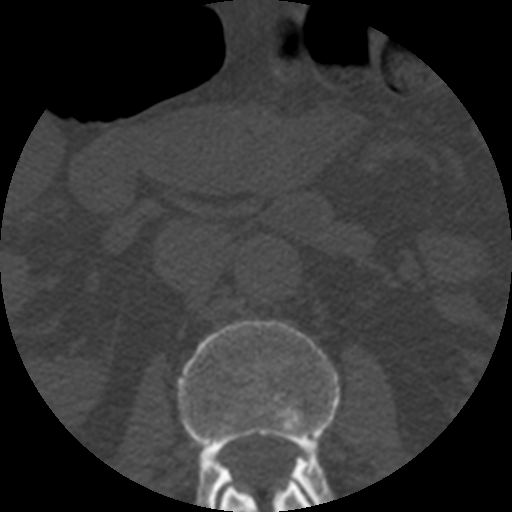
CT including the spine, one axial slice; position 163 of 508 along the scan axis; 120 kVp; bone window (W 1800 / L 400 HU); 1.25 mm slice thickness; 512 × 512 image matrix, field of view 160 × 160 mm. Patient age 57 years. From the clinical record (not read from this slice): primary cancer: prostate.
Outlined on this slice (semi-automatic segmentation, software-assisted and operator-edited):
- L1 vertebra: bounding box <220,482,314,512> (left, top, right, bottom; pixels)
- L2 vertebra: <177,320,340,512>